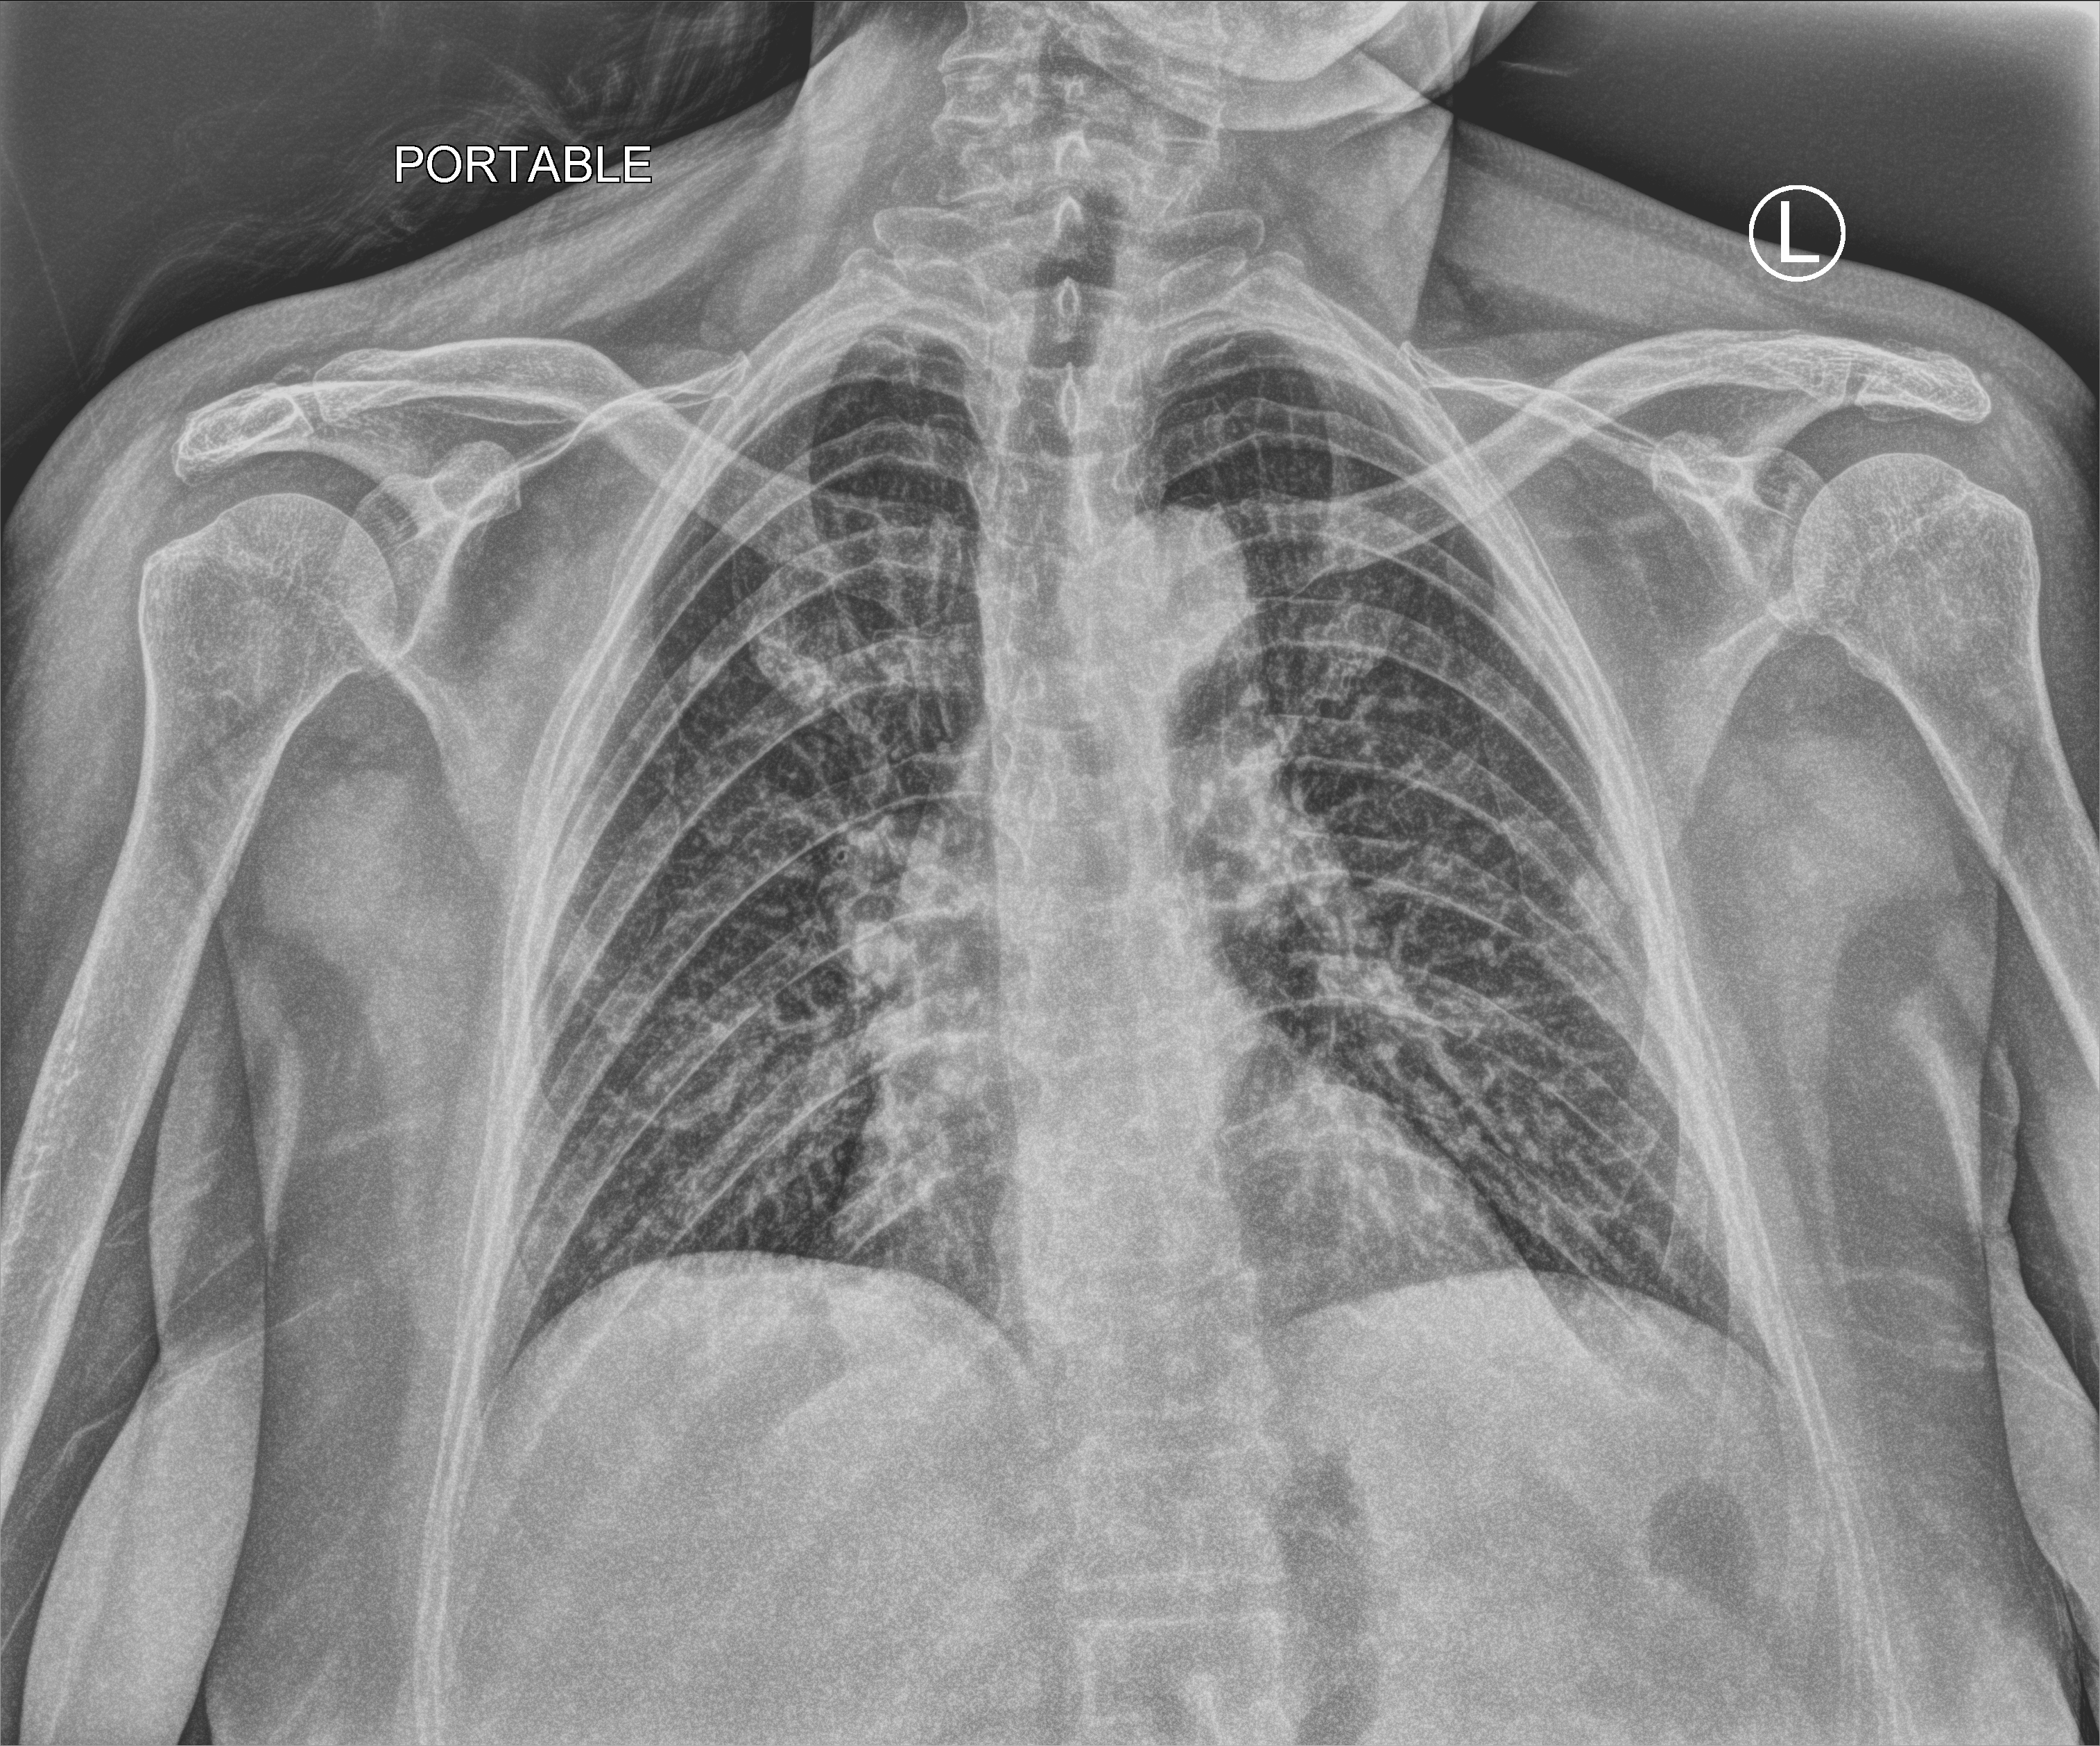
Chest X-ray (portable). Female patient hospitalised with COVID-19, age 60–74 years.
Admission-level facts for this patient (not findings on this image; timing relative to this image not recorded): chronic kidney disease (admission record): no; mechanically ventilated during this hospital stay: no.